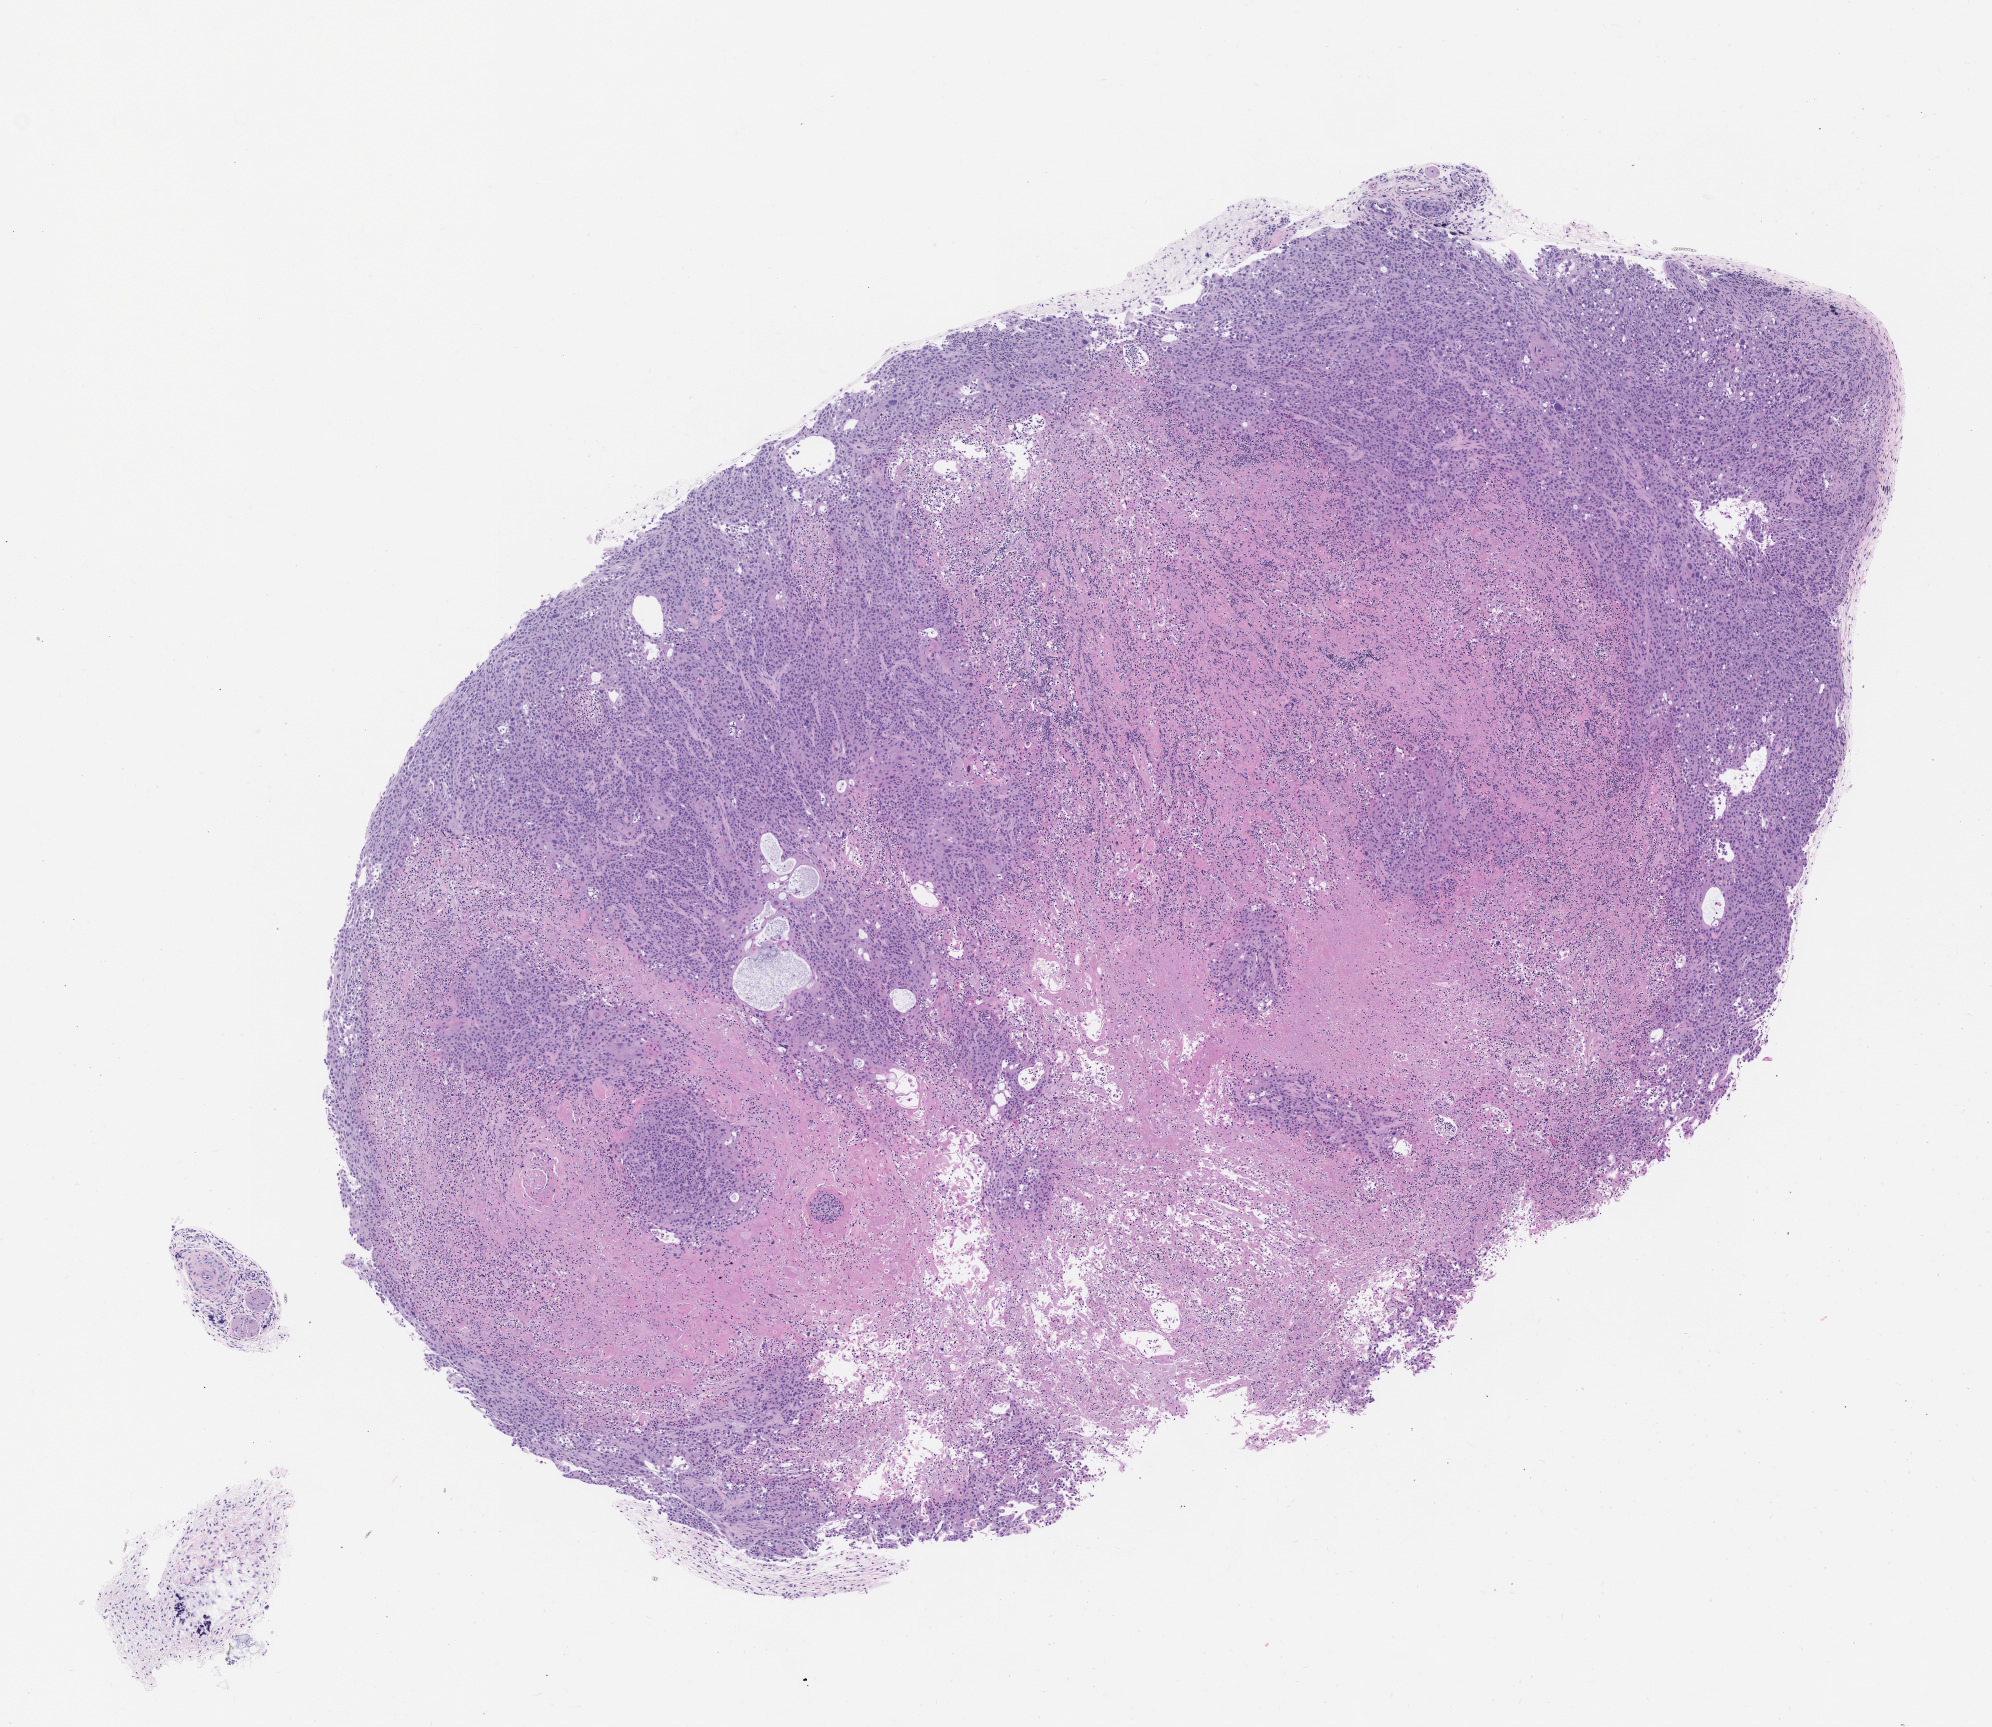
Haematoxylin and eosin whole-slide image of a patient-derived xenograft (PDX) tumor grown in a mouse, passage 0, low-resolution overview of the scanned area, about 8.0 x 6.9 mm. Formalin-fixed paraffin-embedded section. Tumor site category: head and neck.
Originating patient diagnosis: Mucoepidermoid Carcinoma.